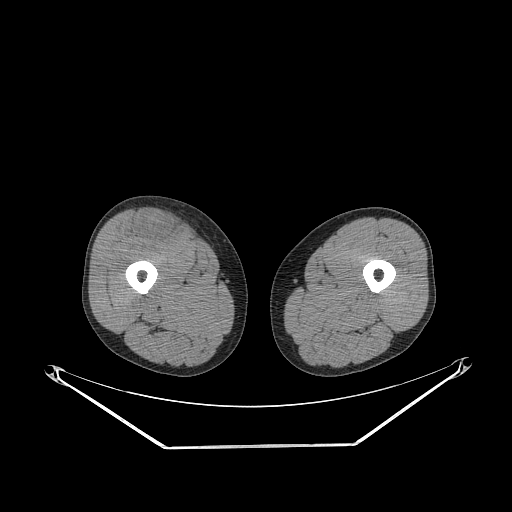
CT of an extremity soft-tissue mass (from a PET/CT study), one axial slice; slice 257 of 311 in the series (ordered by position); reconstruction kernel STANDARD; soft-tissue window (W 400 / L 40 HU); 3.75 mm slice thickness; 512 × 512 image matrix, field of view 500 × 500 mm. Male patient. Case-level facts recorded for this patient, not image findings: histological type: pleiomorphic leiomyosarcoma; grade: intermediate; site of the primary tumour: right thigh.
Structures marked on this image (expert contour drawn on MRI and transferred to this co-registered scan by the dataset authors):
- gross tumour volume including surrounding oedema: bounding box (x1, y1, x2, y2) in pixels: (135, 212, 181, 241)